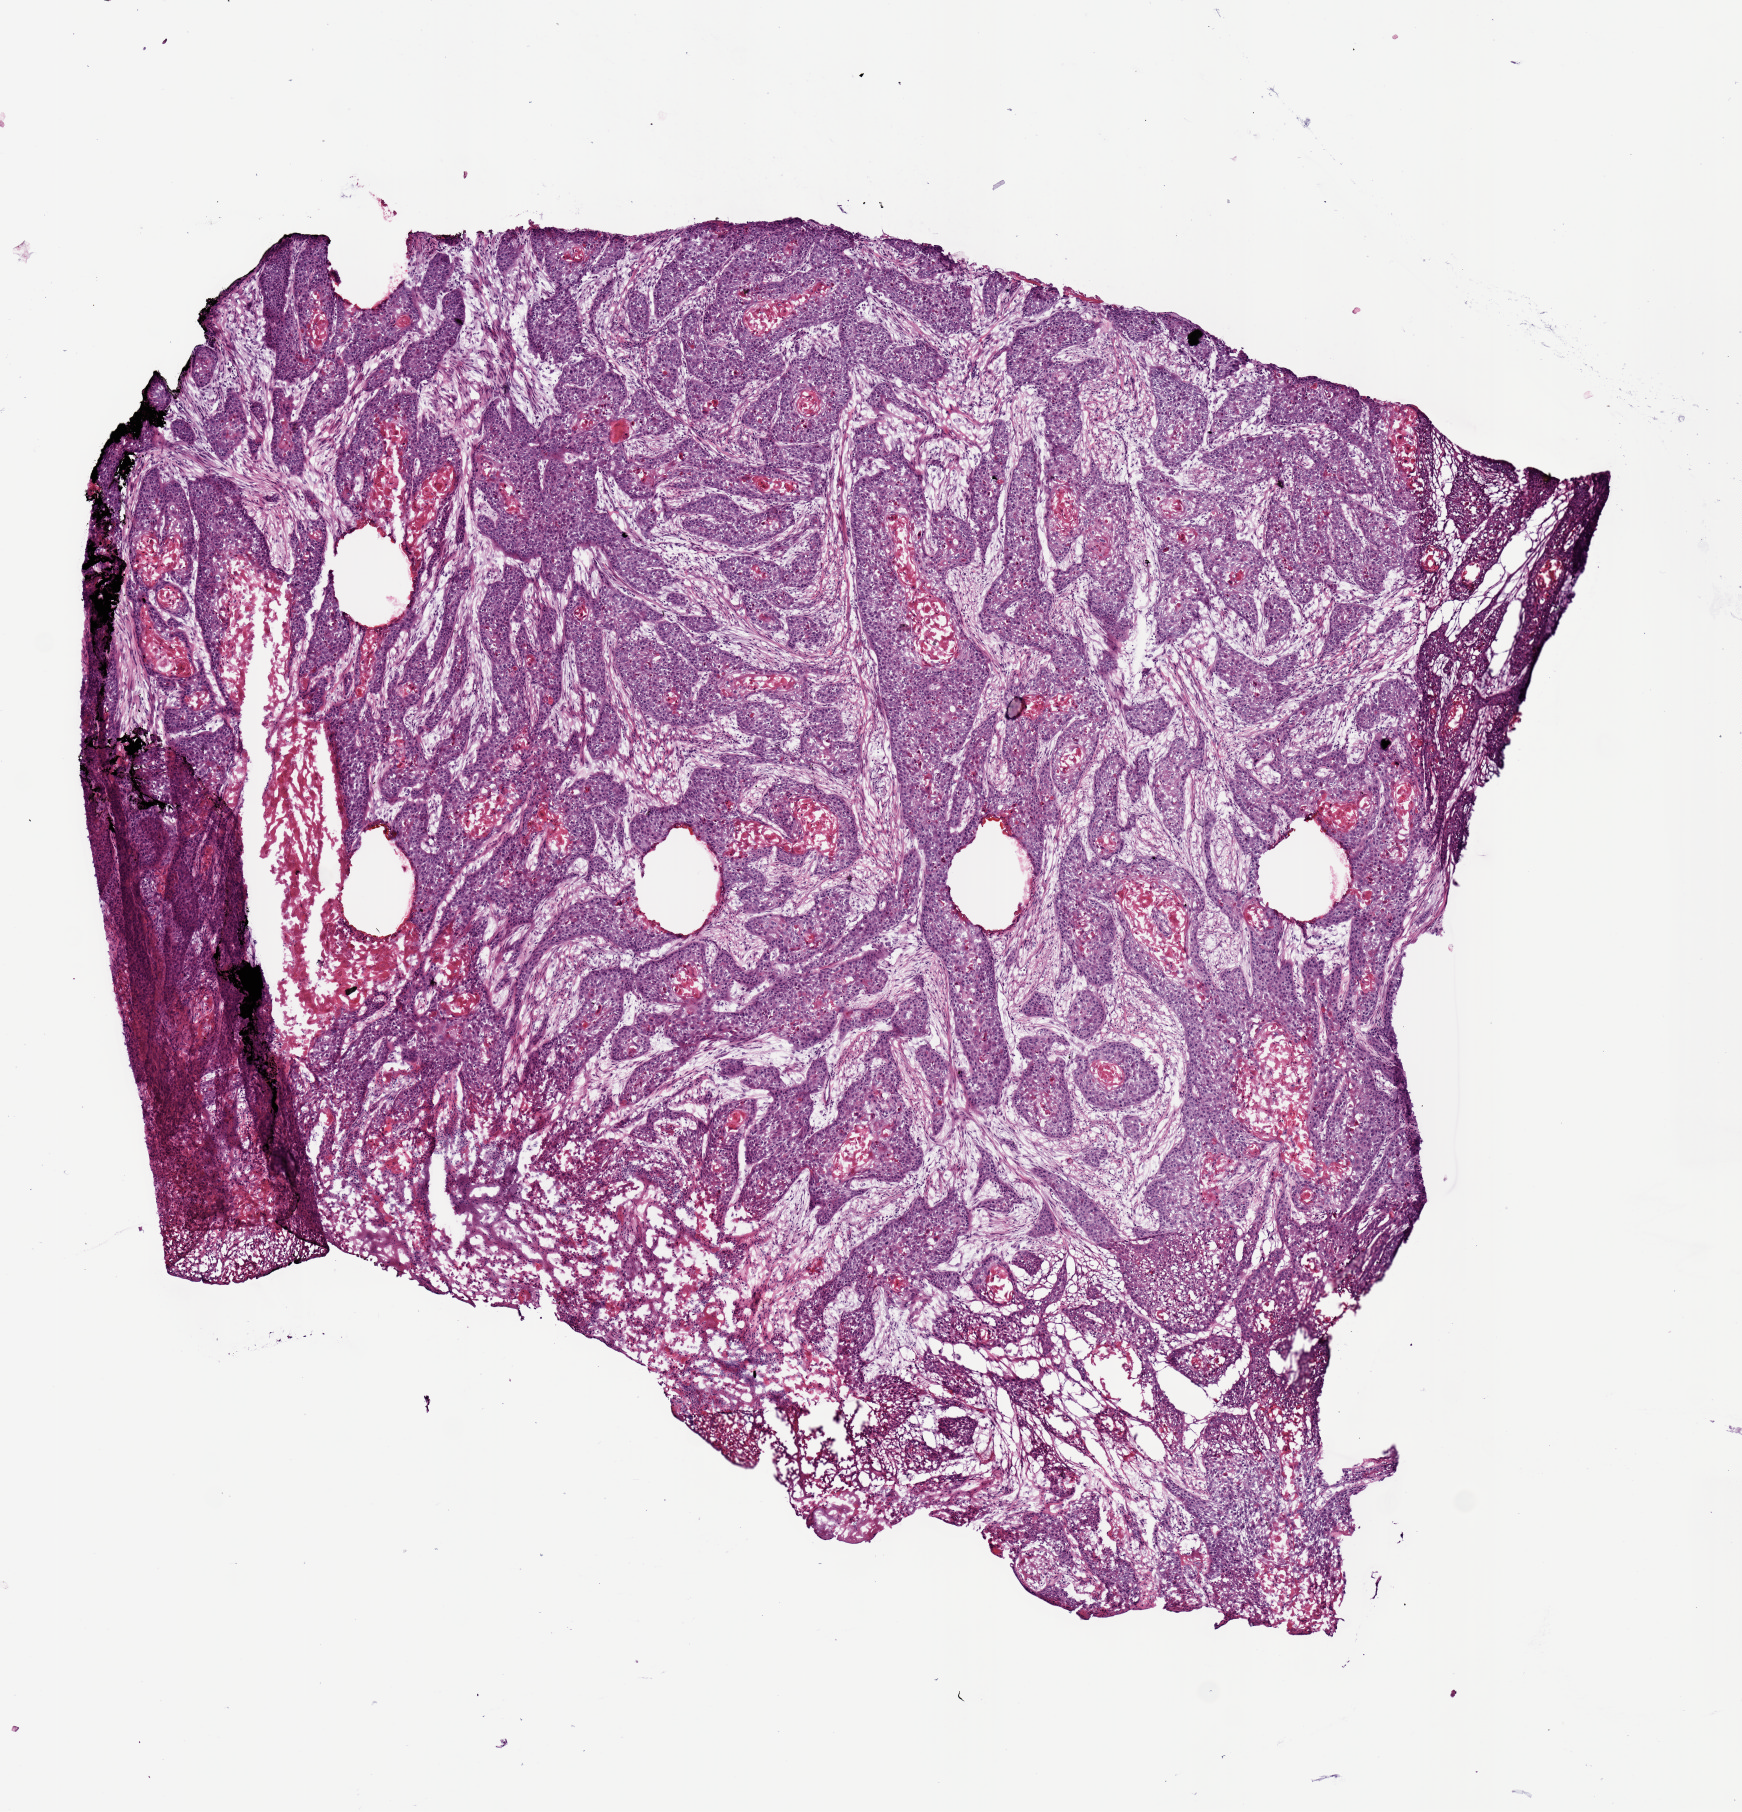
H&E-stained whole-slide image, whole scanned area (about 6.9 x 7.2 mm, slide scanned at 20x) shown as a low-resolution overview. Frozen section. Sample: primary tumour, head and neck. Male, age 52 years at initial diagnosis. Composition of this section per pathologist review: tumour cells 70%, tumour nuclei 75%.
Histologic diagnosis: Squamous cell carcinoma, NOS (floor of mouth, NOS).